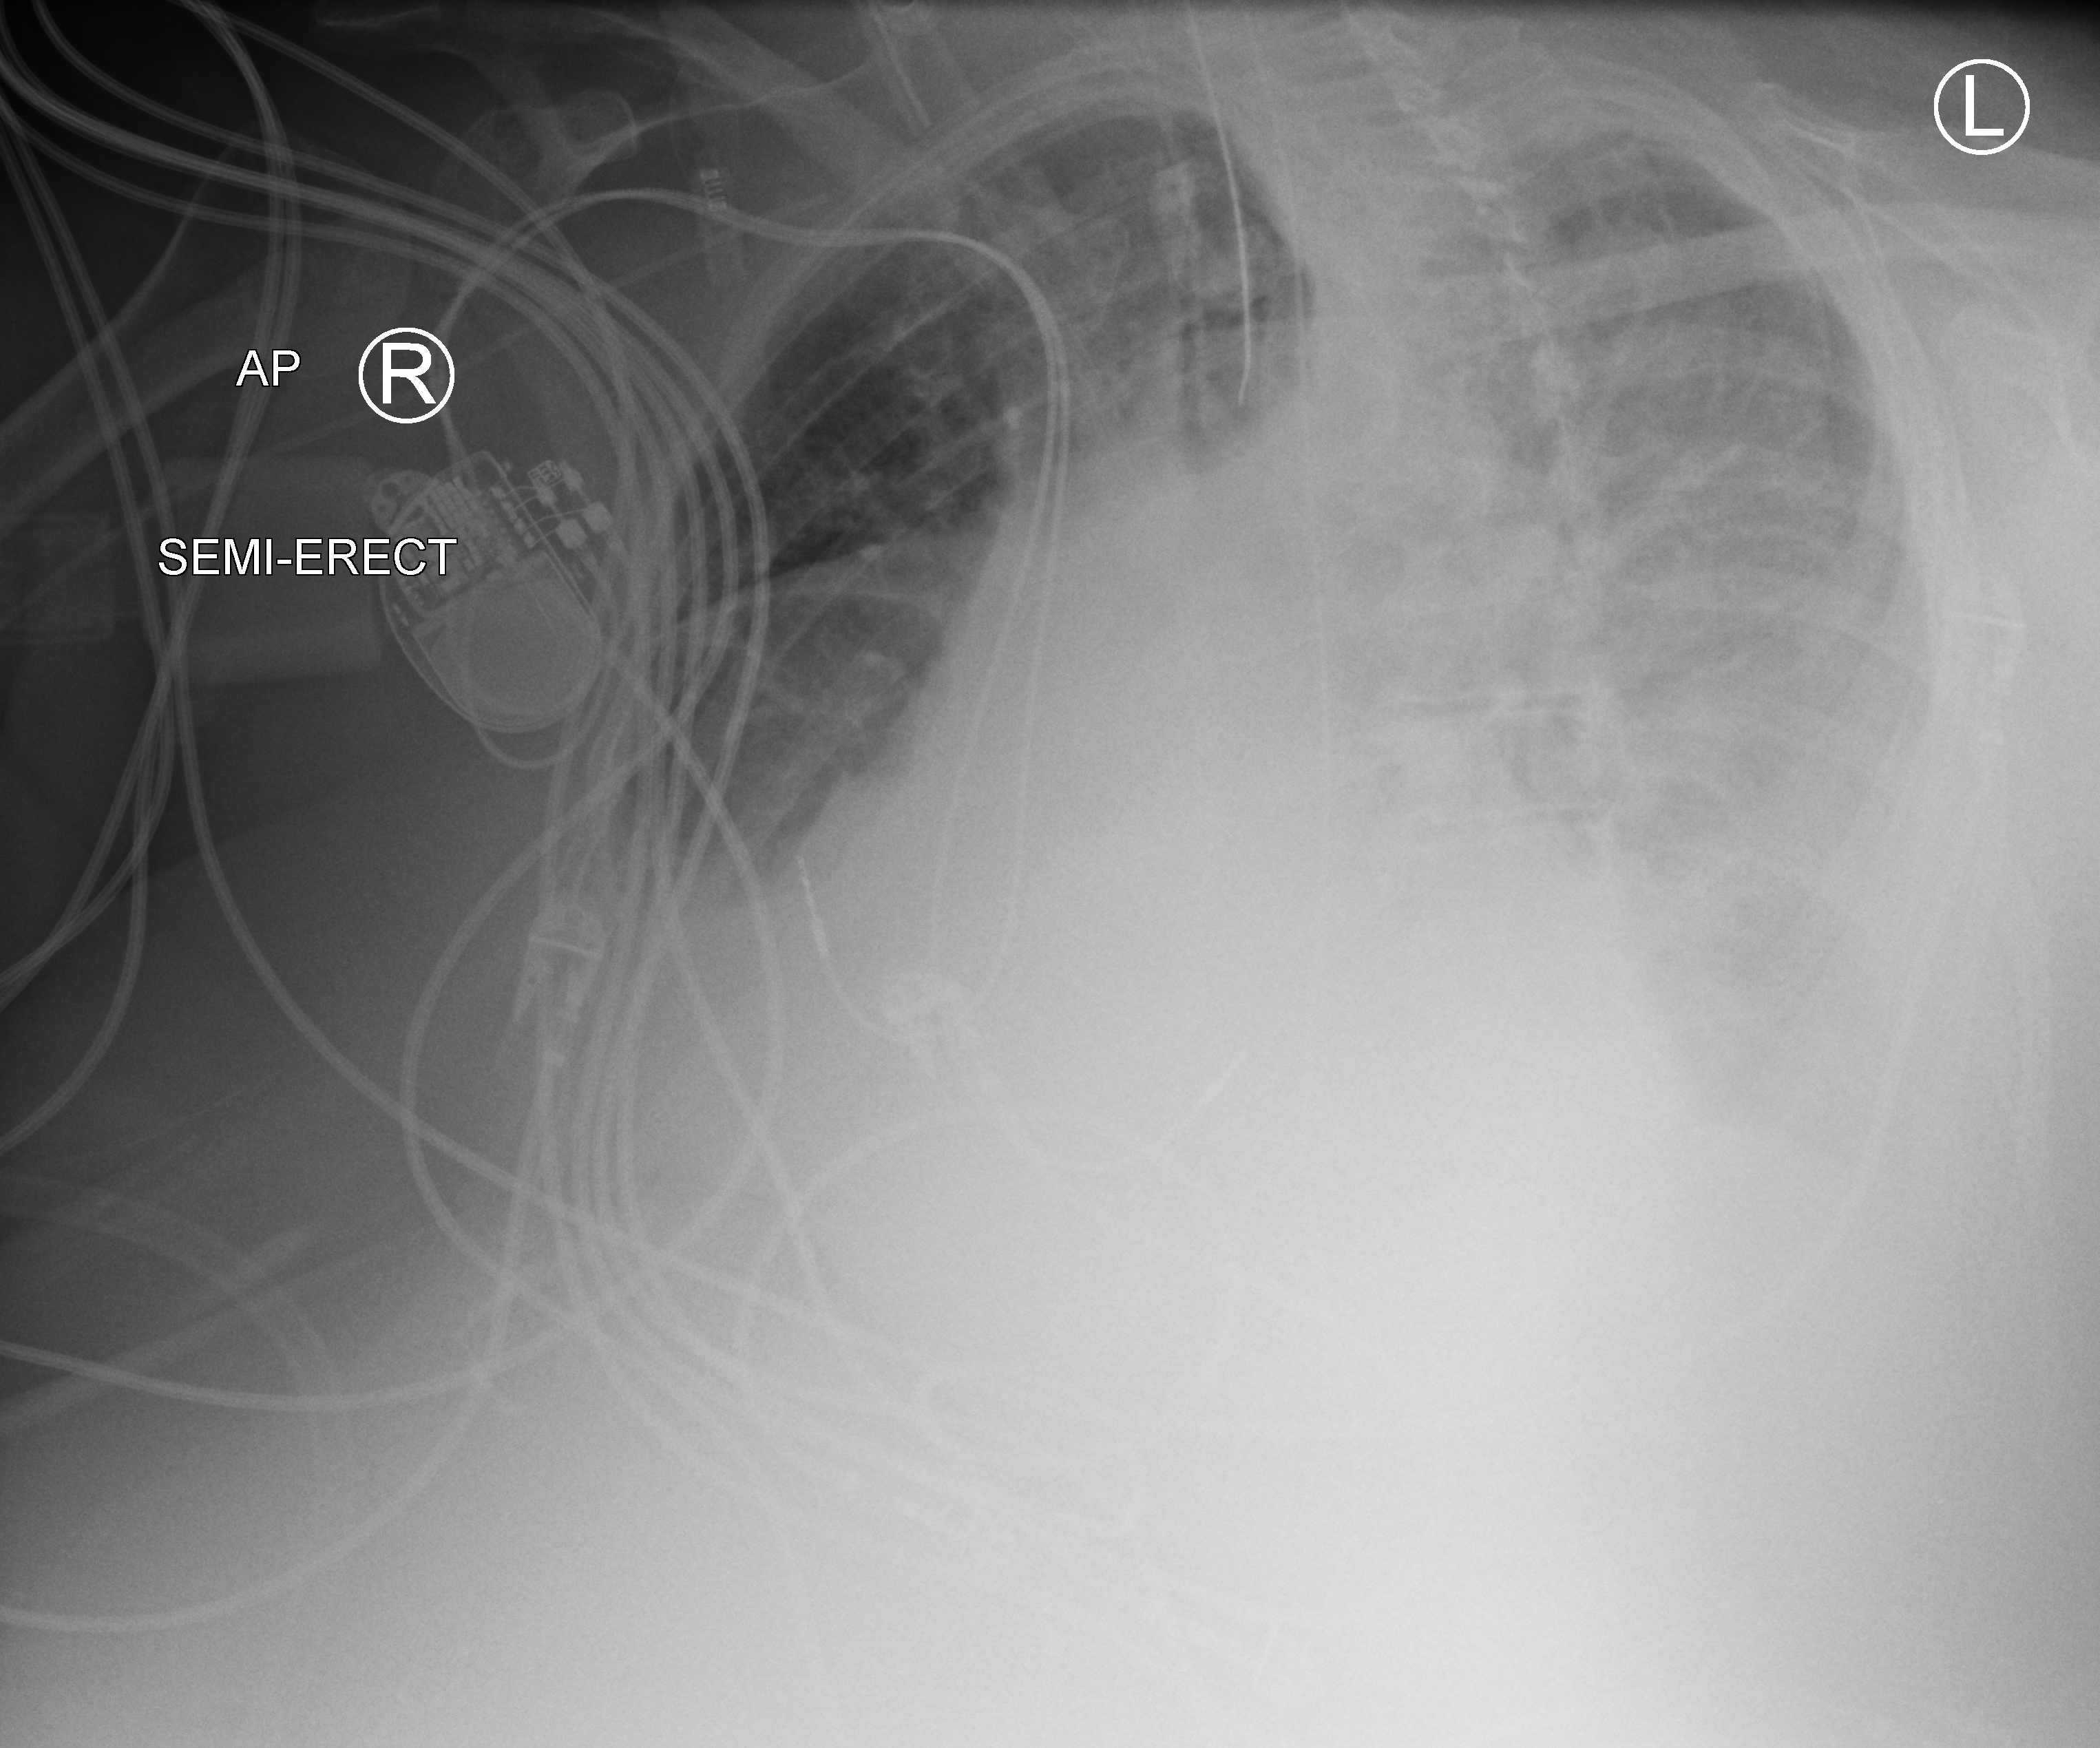
Portable chest radiograph; anteroposterior (AP) projection. Female patient hospitalised with COVID-19, age 75–90 years.
Hospital-stay facts (about this admission, not read from this image; timing relative to this image not recorded): admitted to intensive care during this hospital stay: yes.